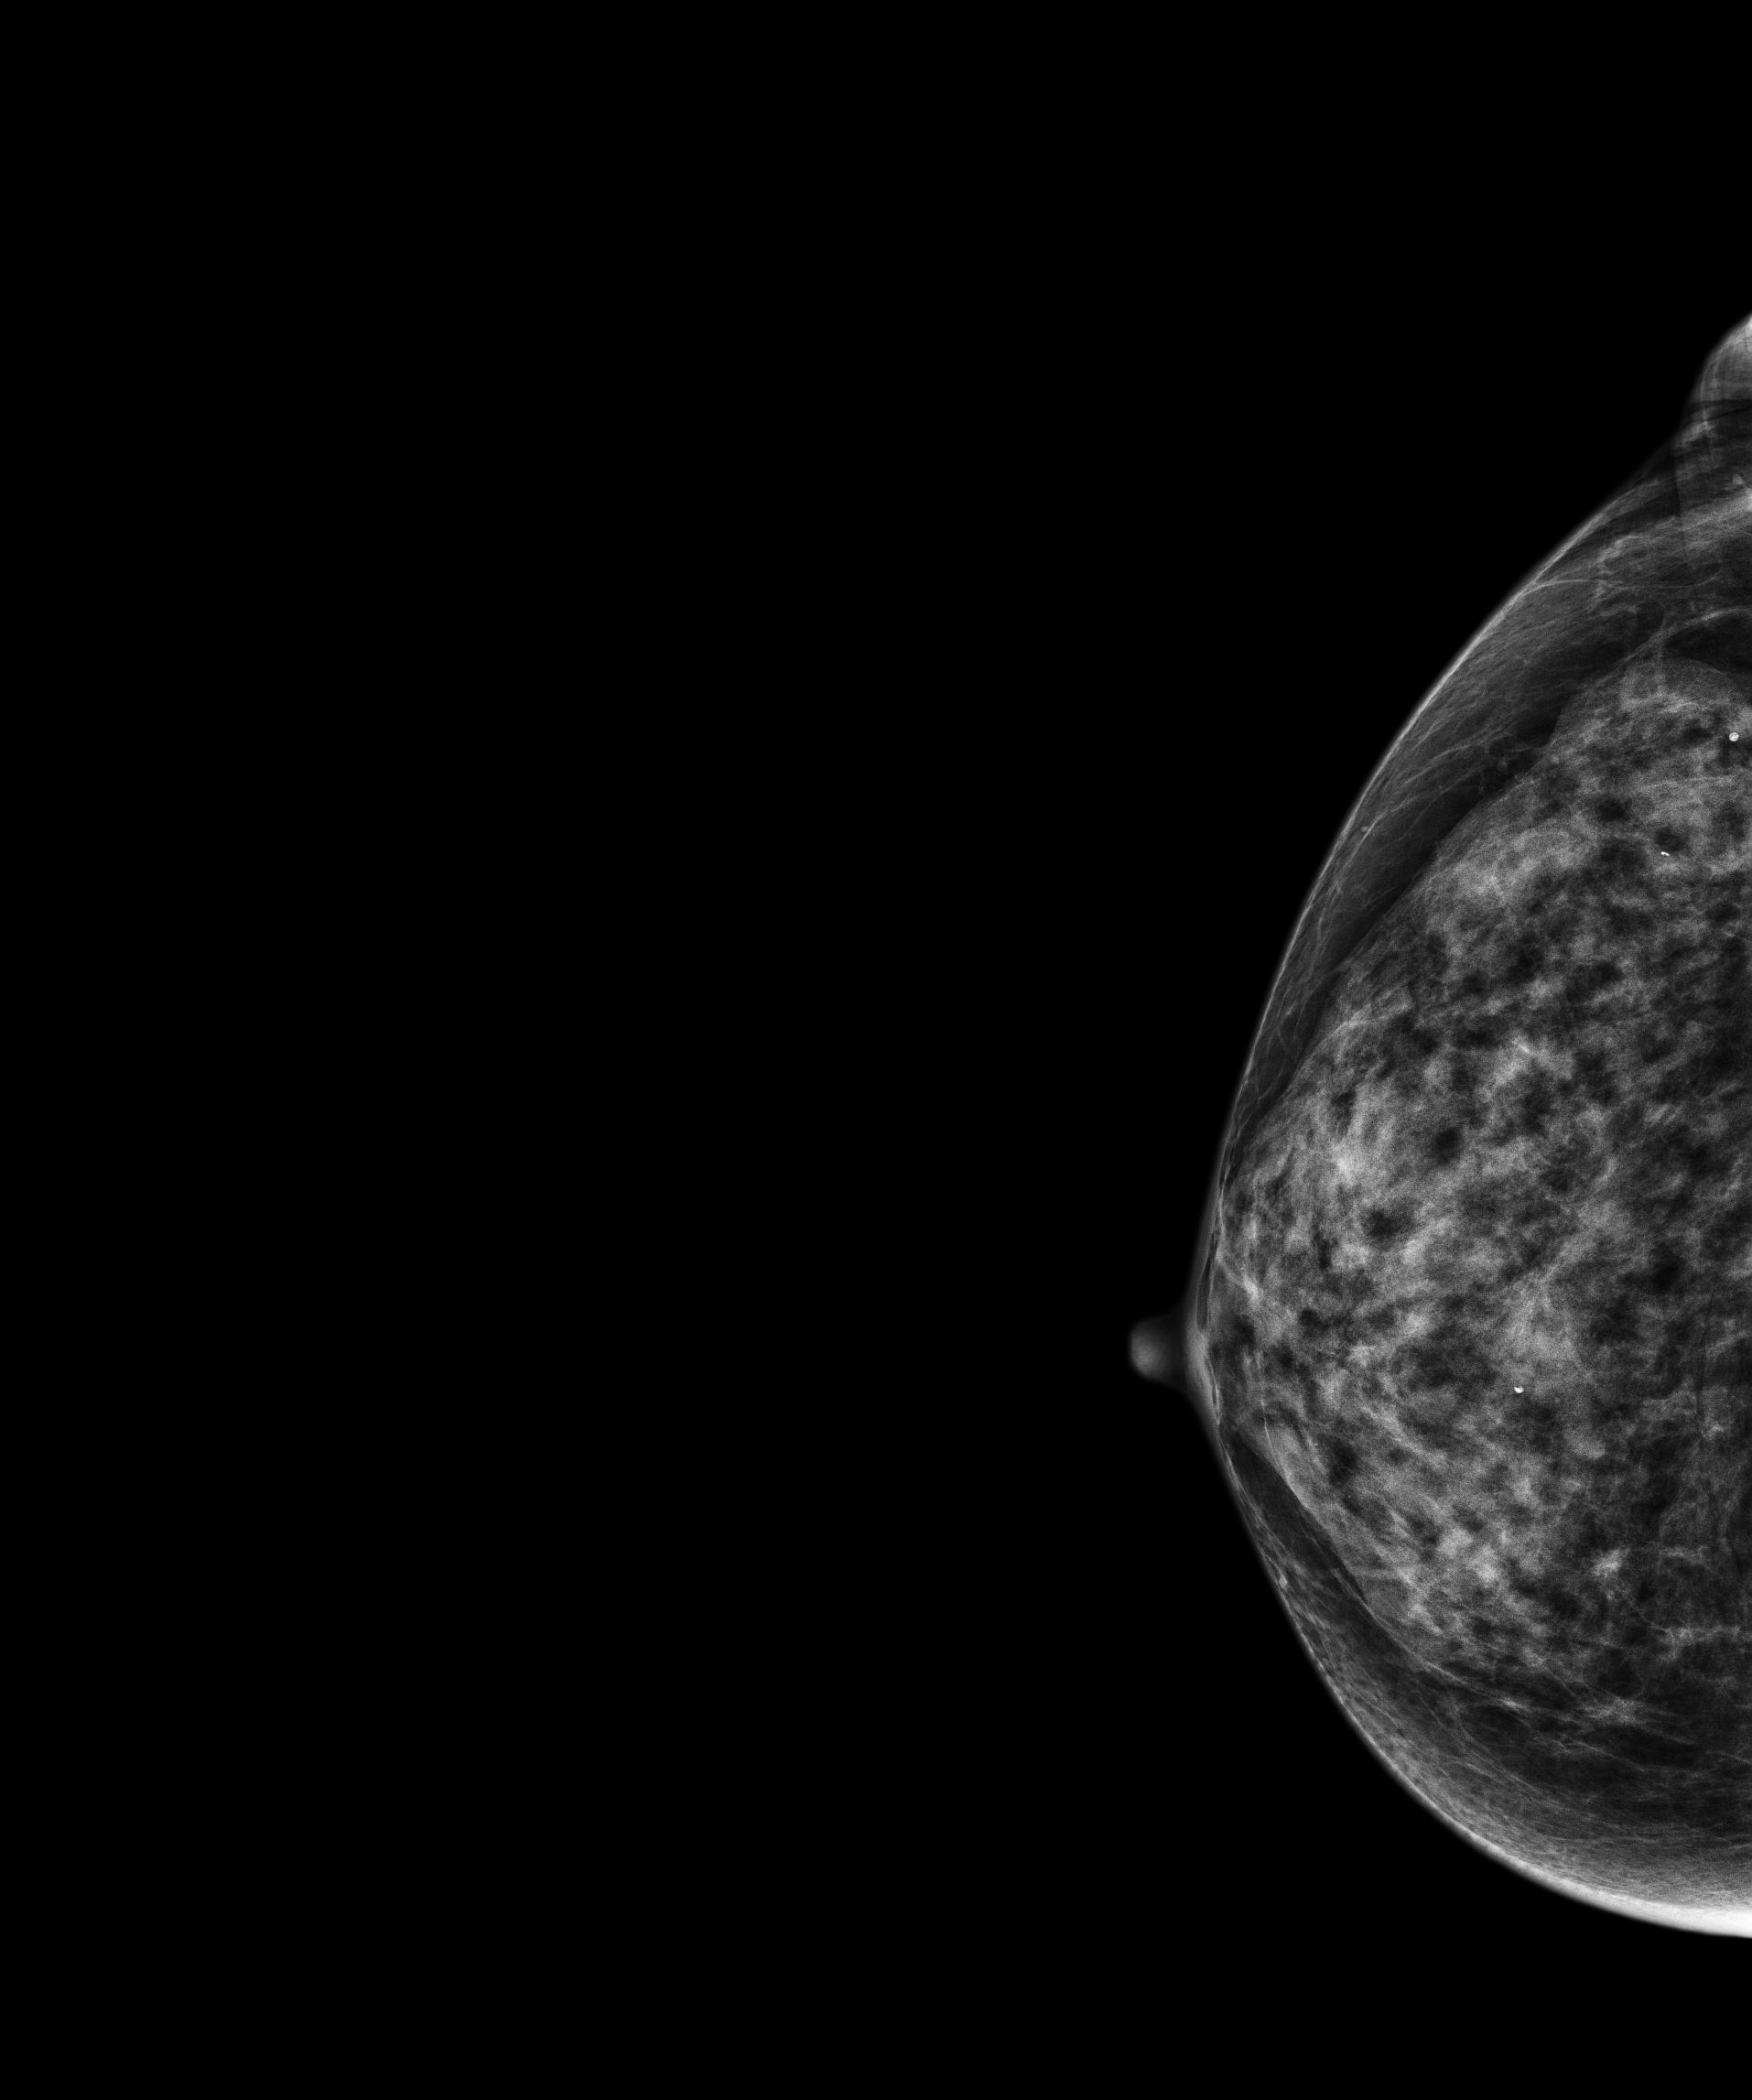
Screening examination, compressed breast thickness 42.9 mm. Patient aged 68 years (female).
Image type: full-field digital mammogram. Breast: right. Projection: craniocaudal (CC) view.